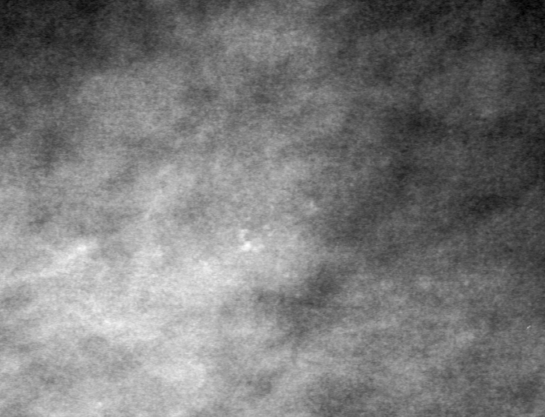
Region of interest cut from a scanned film mammogram (one marked finding), left breast, MLO view, BI-RADS breast density category 3 (scale 1–4).
- Calcifications, morphology pleomorphic, distribution clustered; BI-RADS assessment category 4; pathology result (as recorded, not read from the image): malignant.